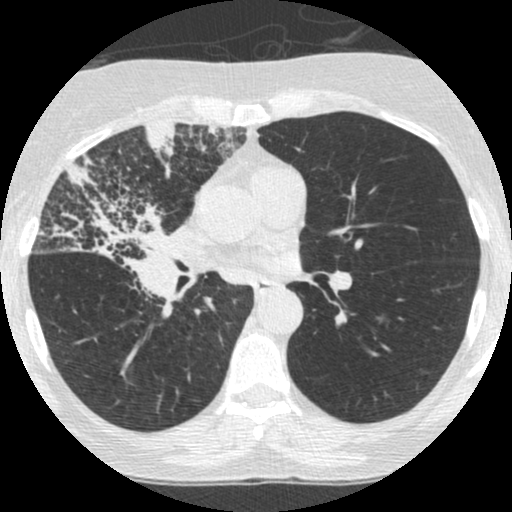
Low-dose screening chest CT, one axial slice. Position 141 of 253 along the scan axis. Reconstruction kernel STANDARD. 120 kVp. Lung window (W 1500 / L -600 HU). 512 × 512 image matrix, field of view 294 × 294 mm.
Structures marked on this image (outlined manually by an expert reader):
- lesion 2 (tumor, hilum of right lung): box from (x=37, y=162) to (x=190, y=317) px
- lesion 3 (tumor, upper lobe of right lung): (x=144, y=122)–(x=177, y=180)
- lesion 4 (tumor, upper lobe of right lung): (x=202, y=125)–(x=241, y=158)